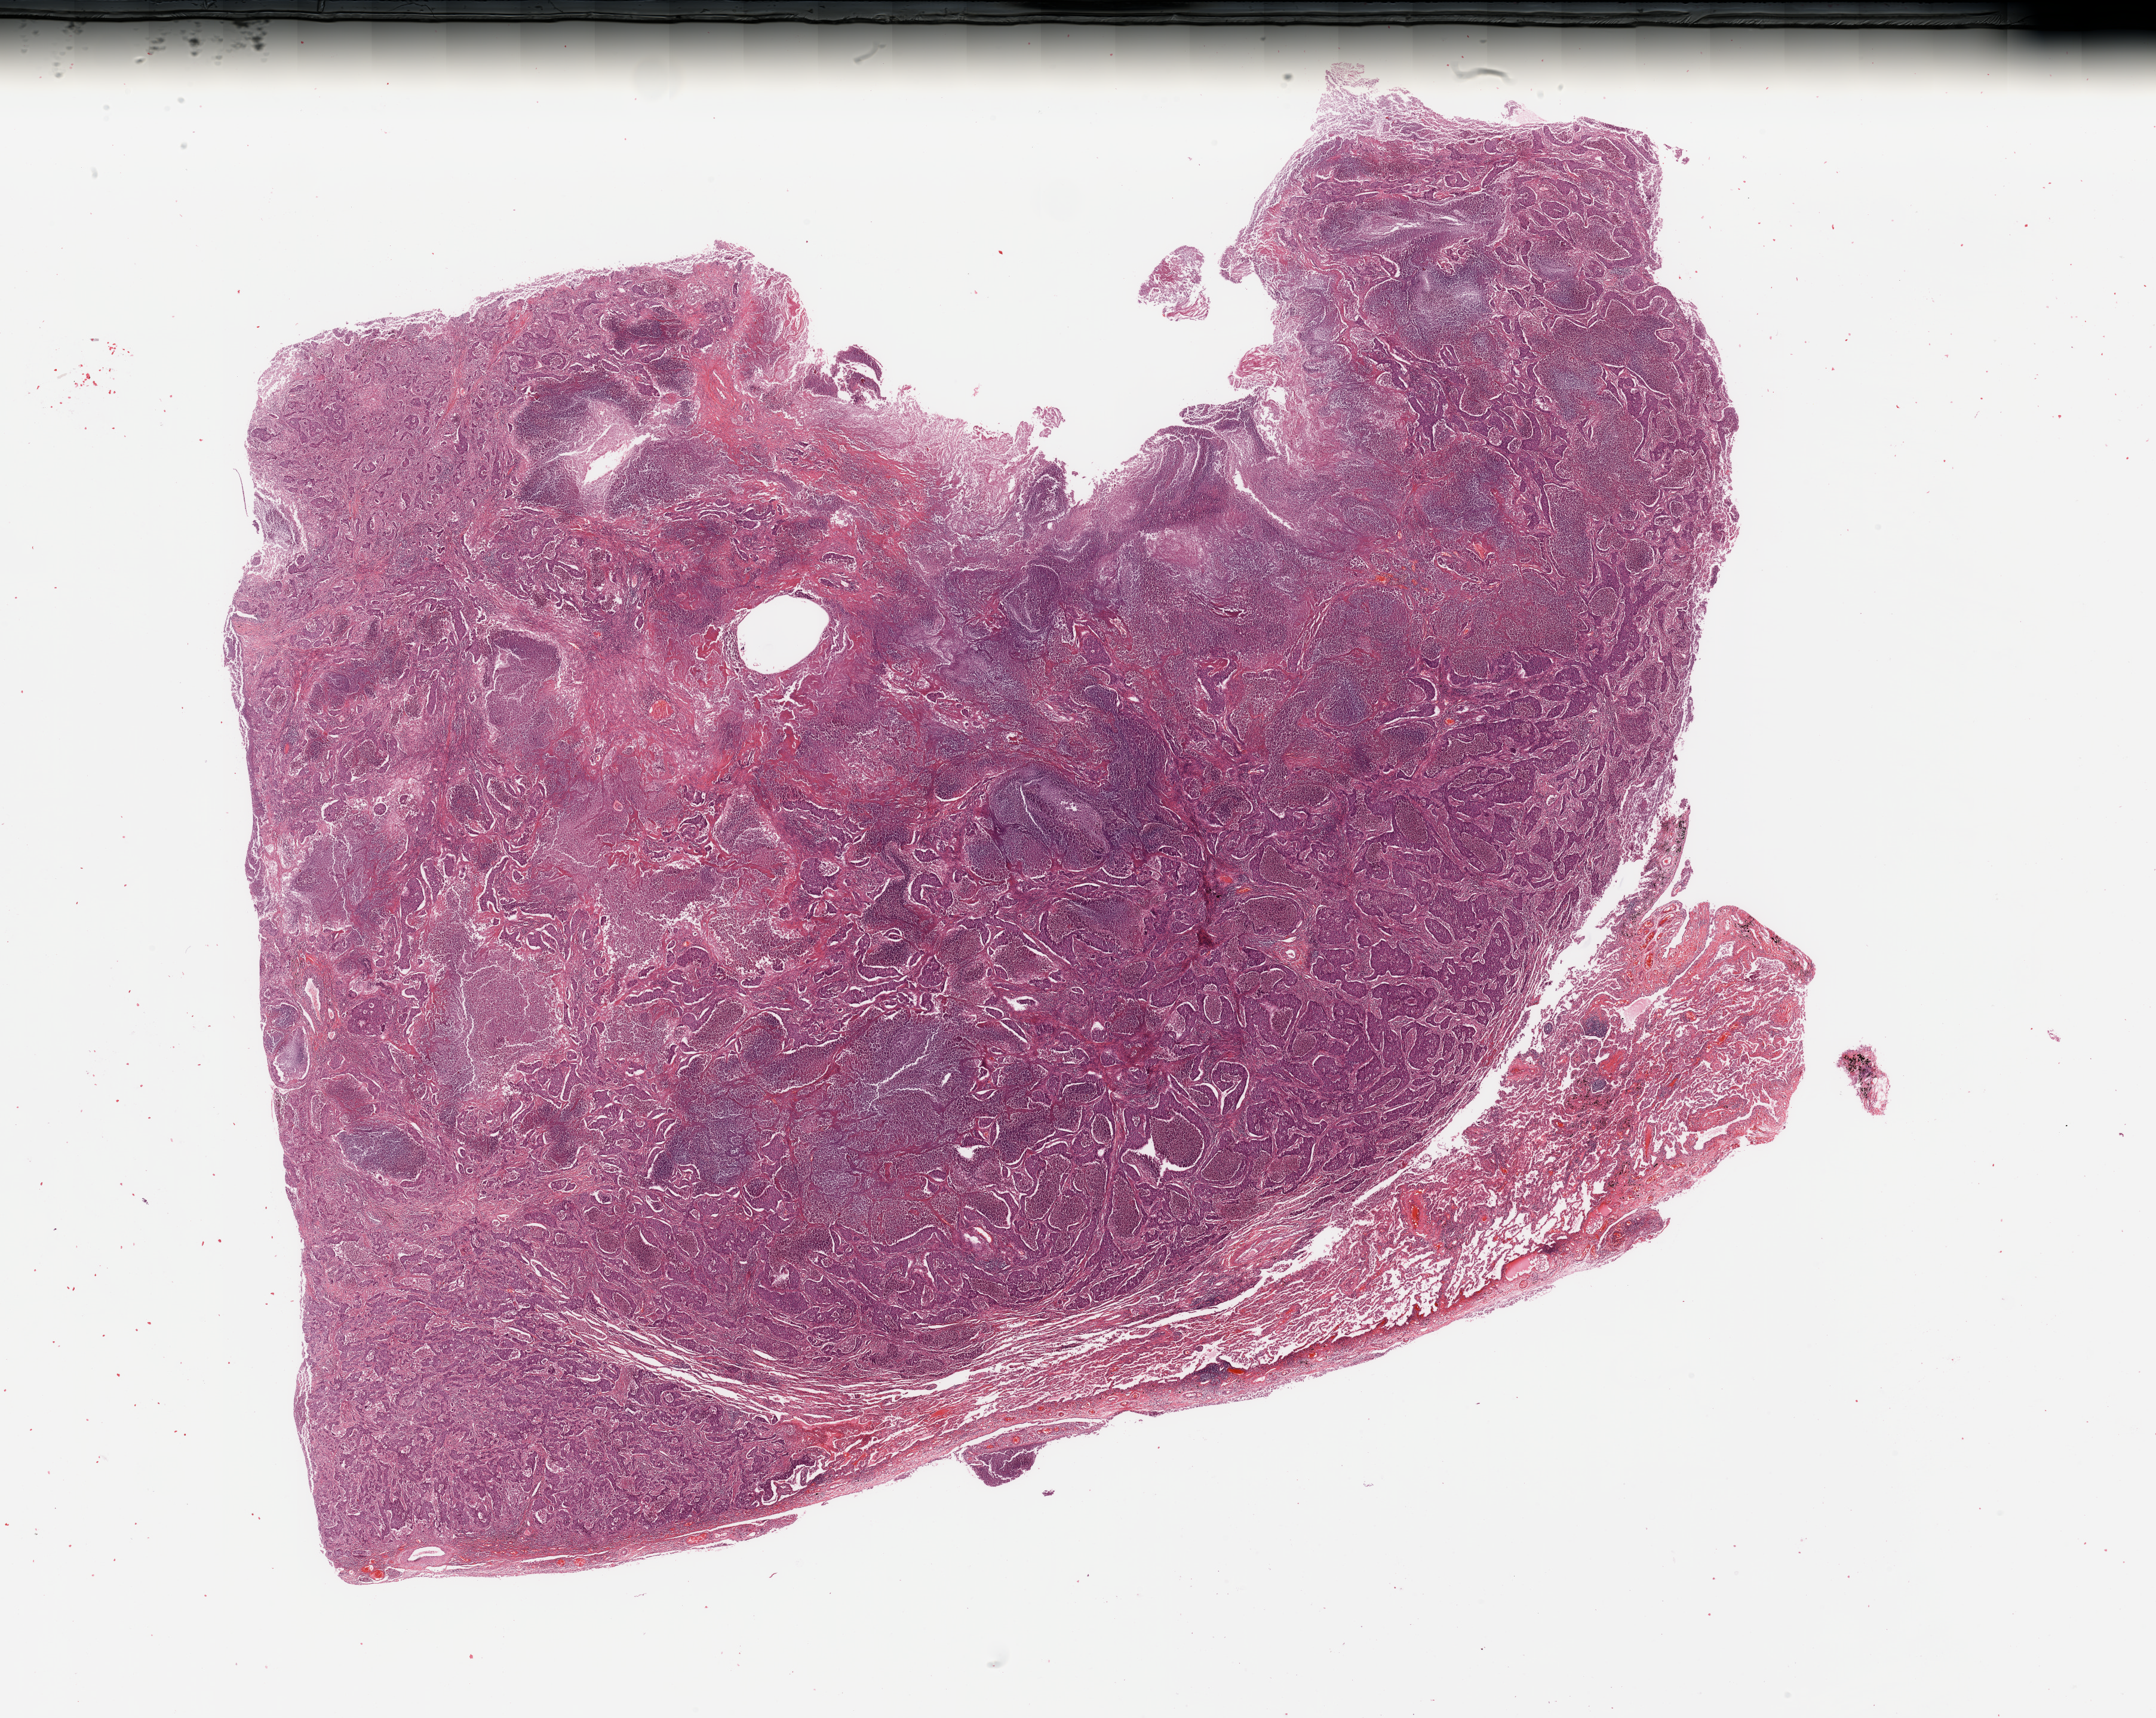
H&E whole-slide image — whole scanned area (about 28.5 x 22.8 mm, slide scanned at 20x) shown as a low-resolution overview; tumour tissue sample, lung. 76-year-old male patient. Histologic grade: G3 (poorly differentiated).
Diagnosis: Adenocarcinoma, NOS. AJCC pathologic stage: IB.